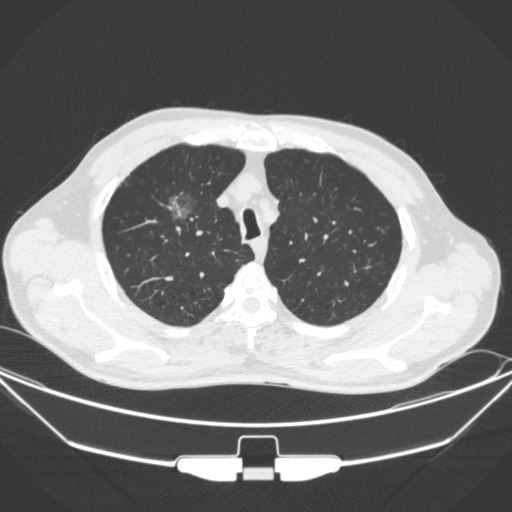
Chest CT, one axial slice; slice 274 of 355 in the series (ordered by position); 120 kVp; lung window (W 1500 / L -600 HU); 1 mm slice thickness; 512 × 512 image matrix, field of view 399 × 399 mm. Male patient, age 67 years. From the clinical record (not read from this slice): clinical TNM (as recorded): T1c N0 M0; histopathological grade: G2.
Outlined on this slice (bounding box drawn by a radiologist):
- lung tumour (recorded histology: adenocarcinoma): box from (x=158, y=186) to (x=204, y=230) px